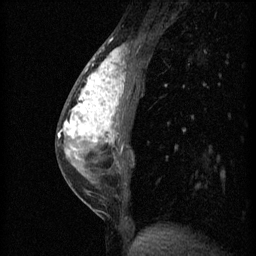
Breast MRI (dynamic contrast-enhanced), one sagittal slice; slice 22 of 60 in the series (ordered by position); 3 images stored at this slice position (order not interpretable as contrast timing); 1.5 T; TE 4.2 ms, TR 11 ms; 2 mm slice thickness; 256 × 256 image matrix, field of view 180 × 180 mm. Patient: female, 40 years.
Structures marked on this image (semi-automatically segmented with operator editing):
- analysis volume of interest (the breast-tissue region the enhancement analysis was run in; not a lesion): bounding box [x1, y1, x2, y2] px = [57, 42, 141, 203]
- tumour enhancement mask (voxels above the 70 % enhancement threshold inside the analysis volume of interest): [58, 48, 125, 159]